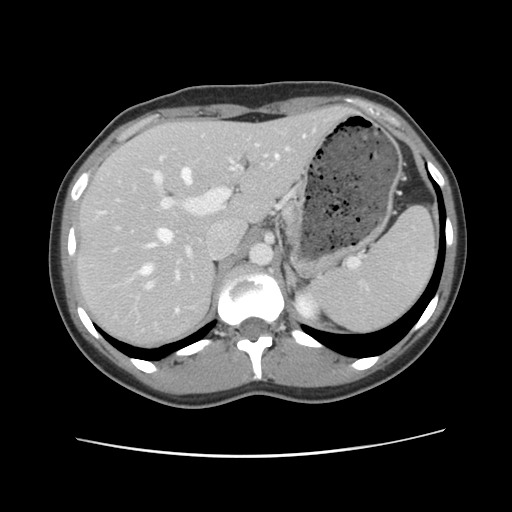
Contrast-enhanced abdominal CT, one axial slice; slice 76 of 134 in the series (ordered by position); 120 kVp; intravenous contrast given; soft-tissue window (W 400 / L 40 HU); 512 × 512 image matrix, field of view 339 × 339 mm. Female patient, age 33 years. Case-level facts recorded for this patient, not image findings: diagnosis: colorectal cancer liver metastases, imaged before liver resection; multiple liver metastases: yes; largest metastasis: 4.5 cm; chemotherapy before resection: no.
Annotated regions visible in this slice (manually delineated by an expert):
- hepatic veins: box from (x=101, y=136) to (x=305, y=313) px
- liver: (x=78, y=107)–(x=349, y=349)
- planned liver remnant (the part of the liver to remain after resection): (x=78, y=108)–(x=350, y=349)
- portal vein (with intrahepatic branches): (x=150, y=146)–(x=292, y=286)